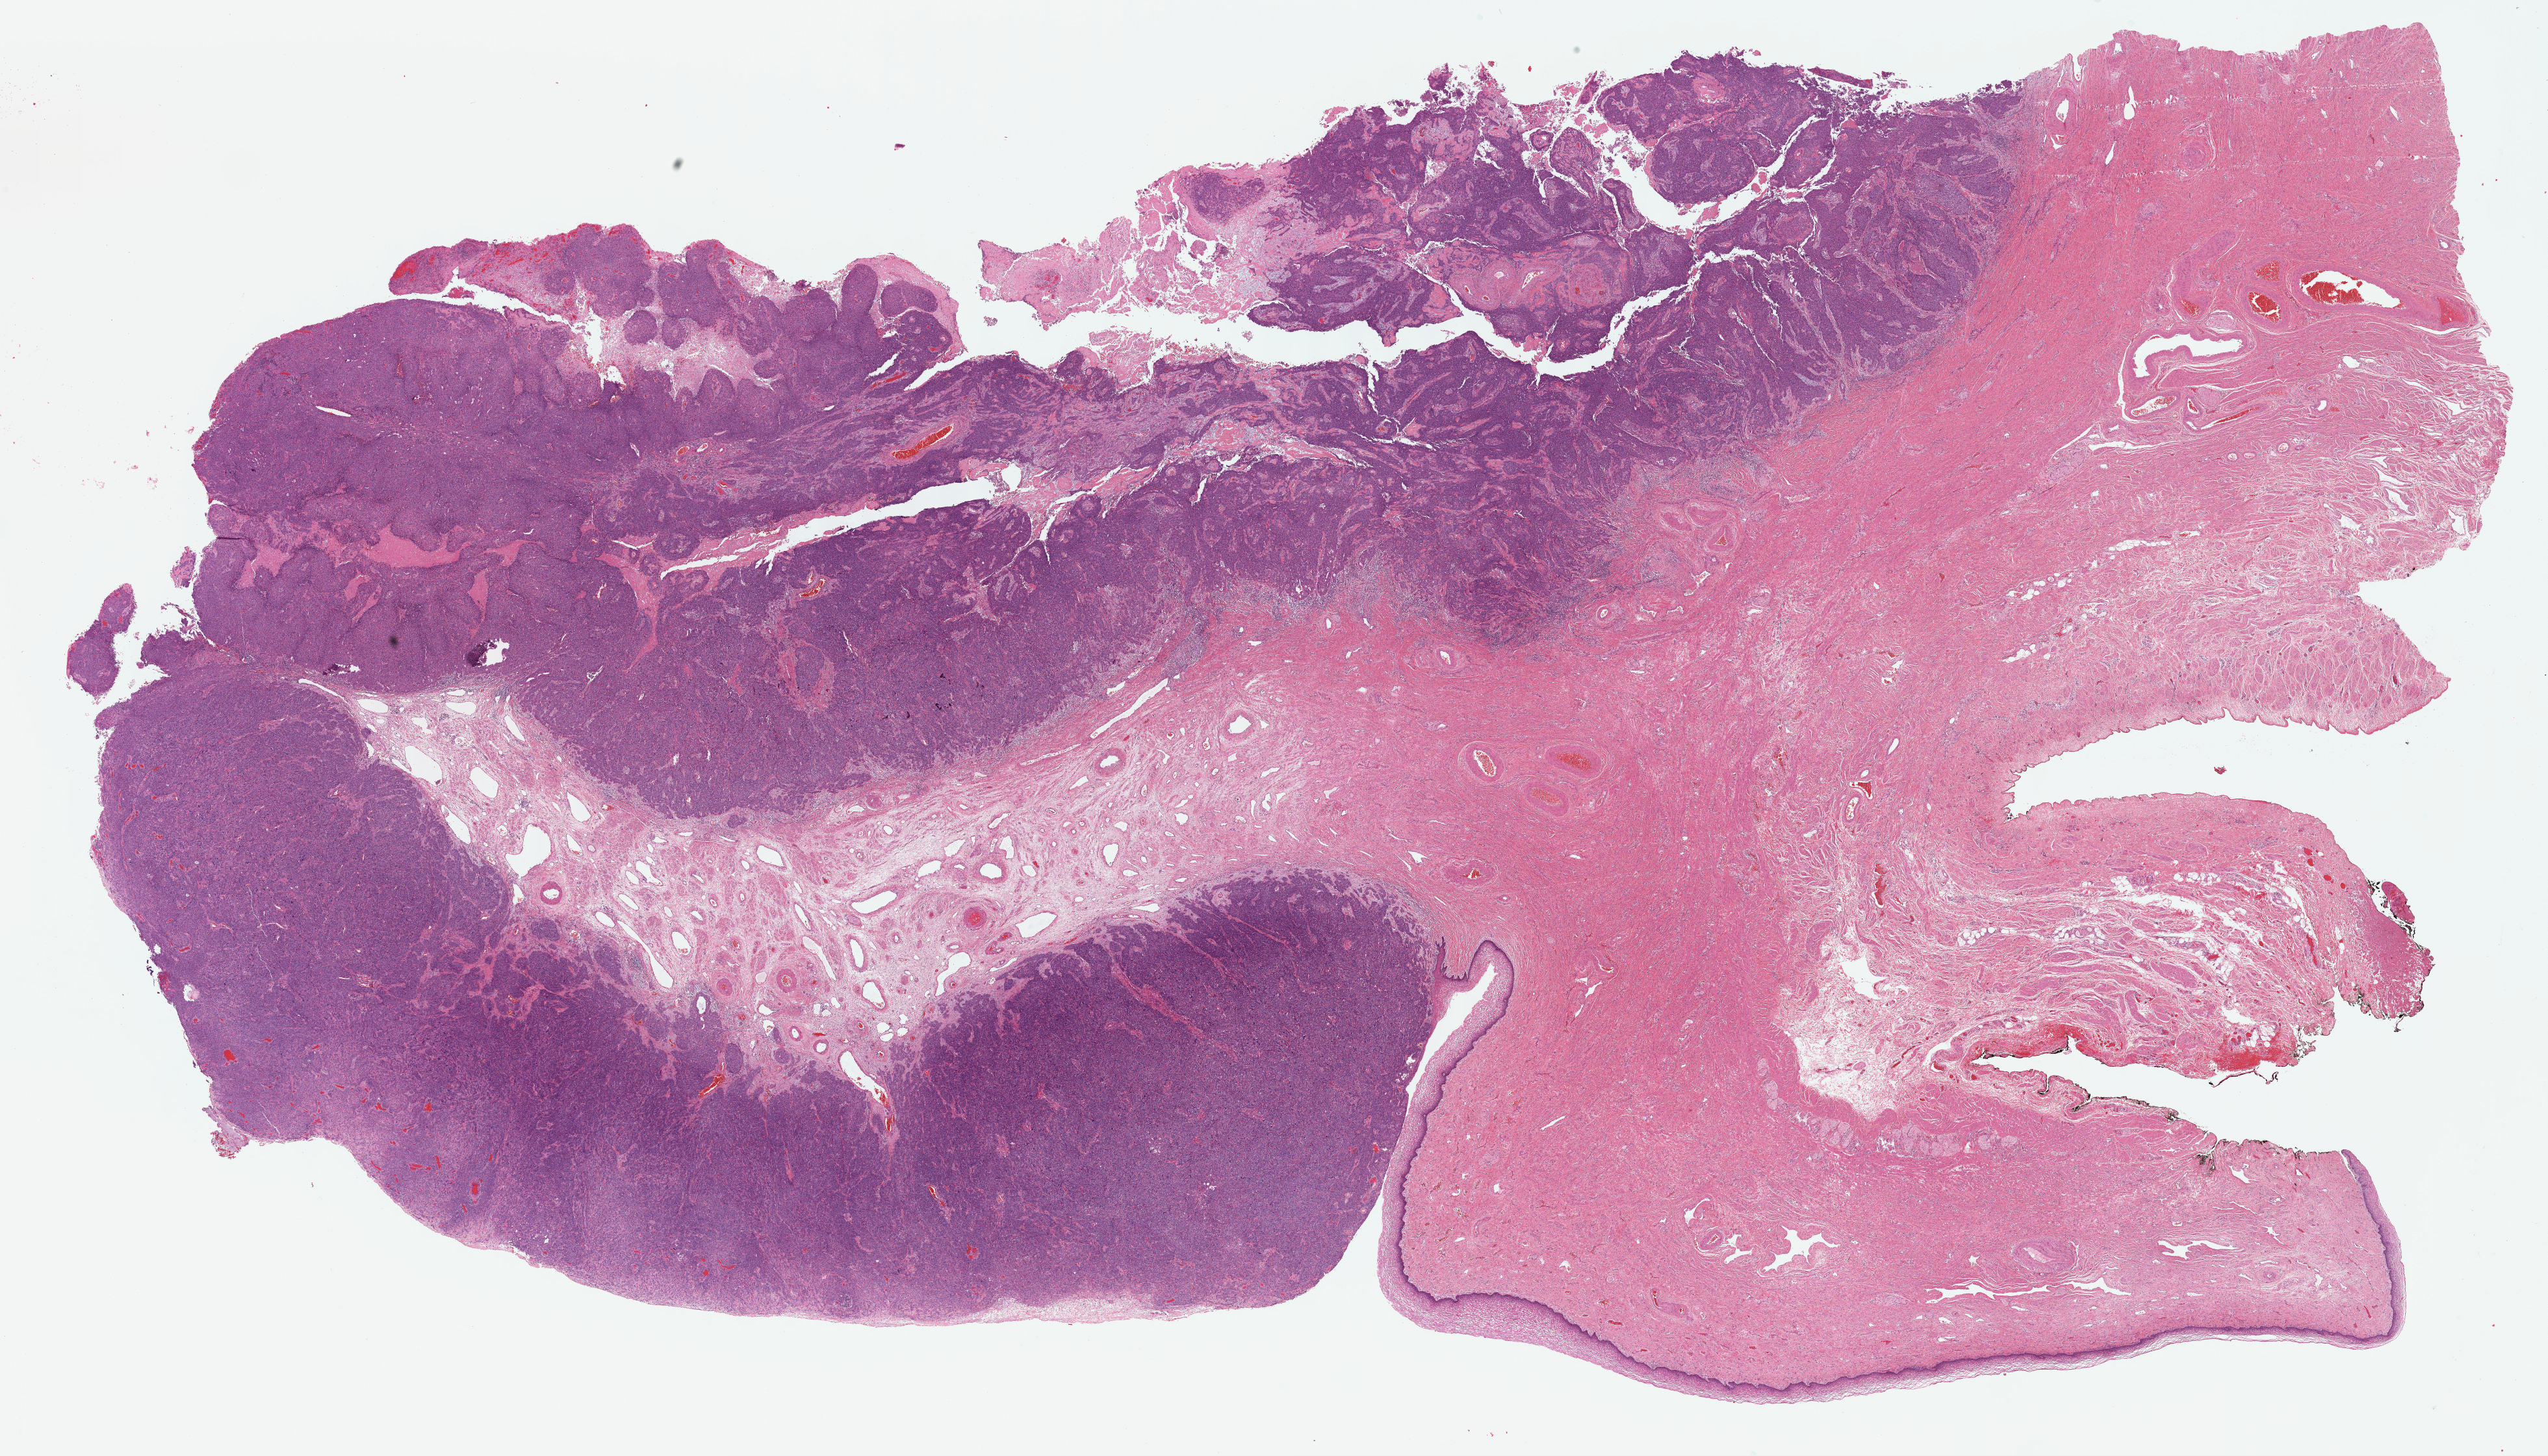
H&E whole-slide image — a low-resolution overview of the entire scanned area, about 31.7 x 18.1 mm (slide scanned at 40x), formalin-fixed paraffin-embedded (FFPE) diagnostic section, sample: primary tumour, cervix. Female patient; age at initial diagnosis 41 years. Histologic grade: G3 (poorly differentiated).
* FIGO stage: IB2
* pathologic diagnosis: Adenosquamous carcinoma (cervix uteri)
* lymph nodes positive (case pathology): 0 of 23 examined